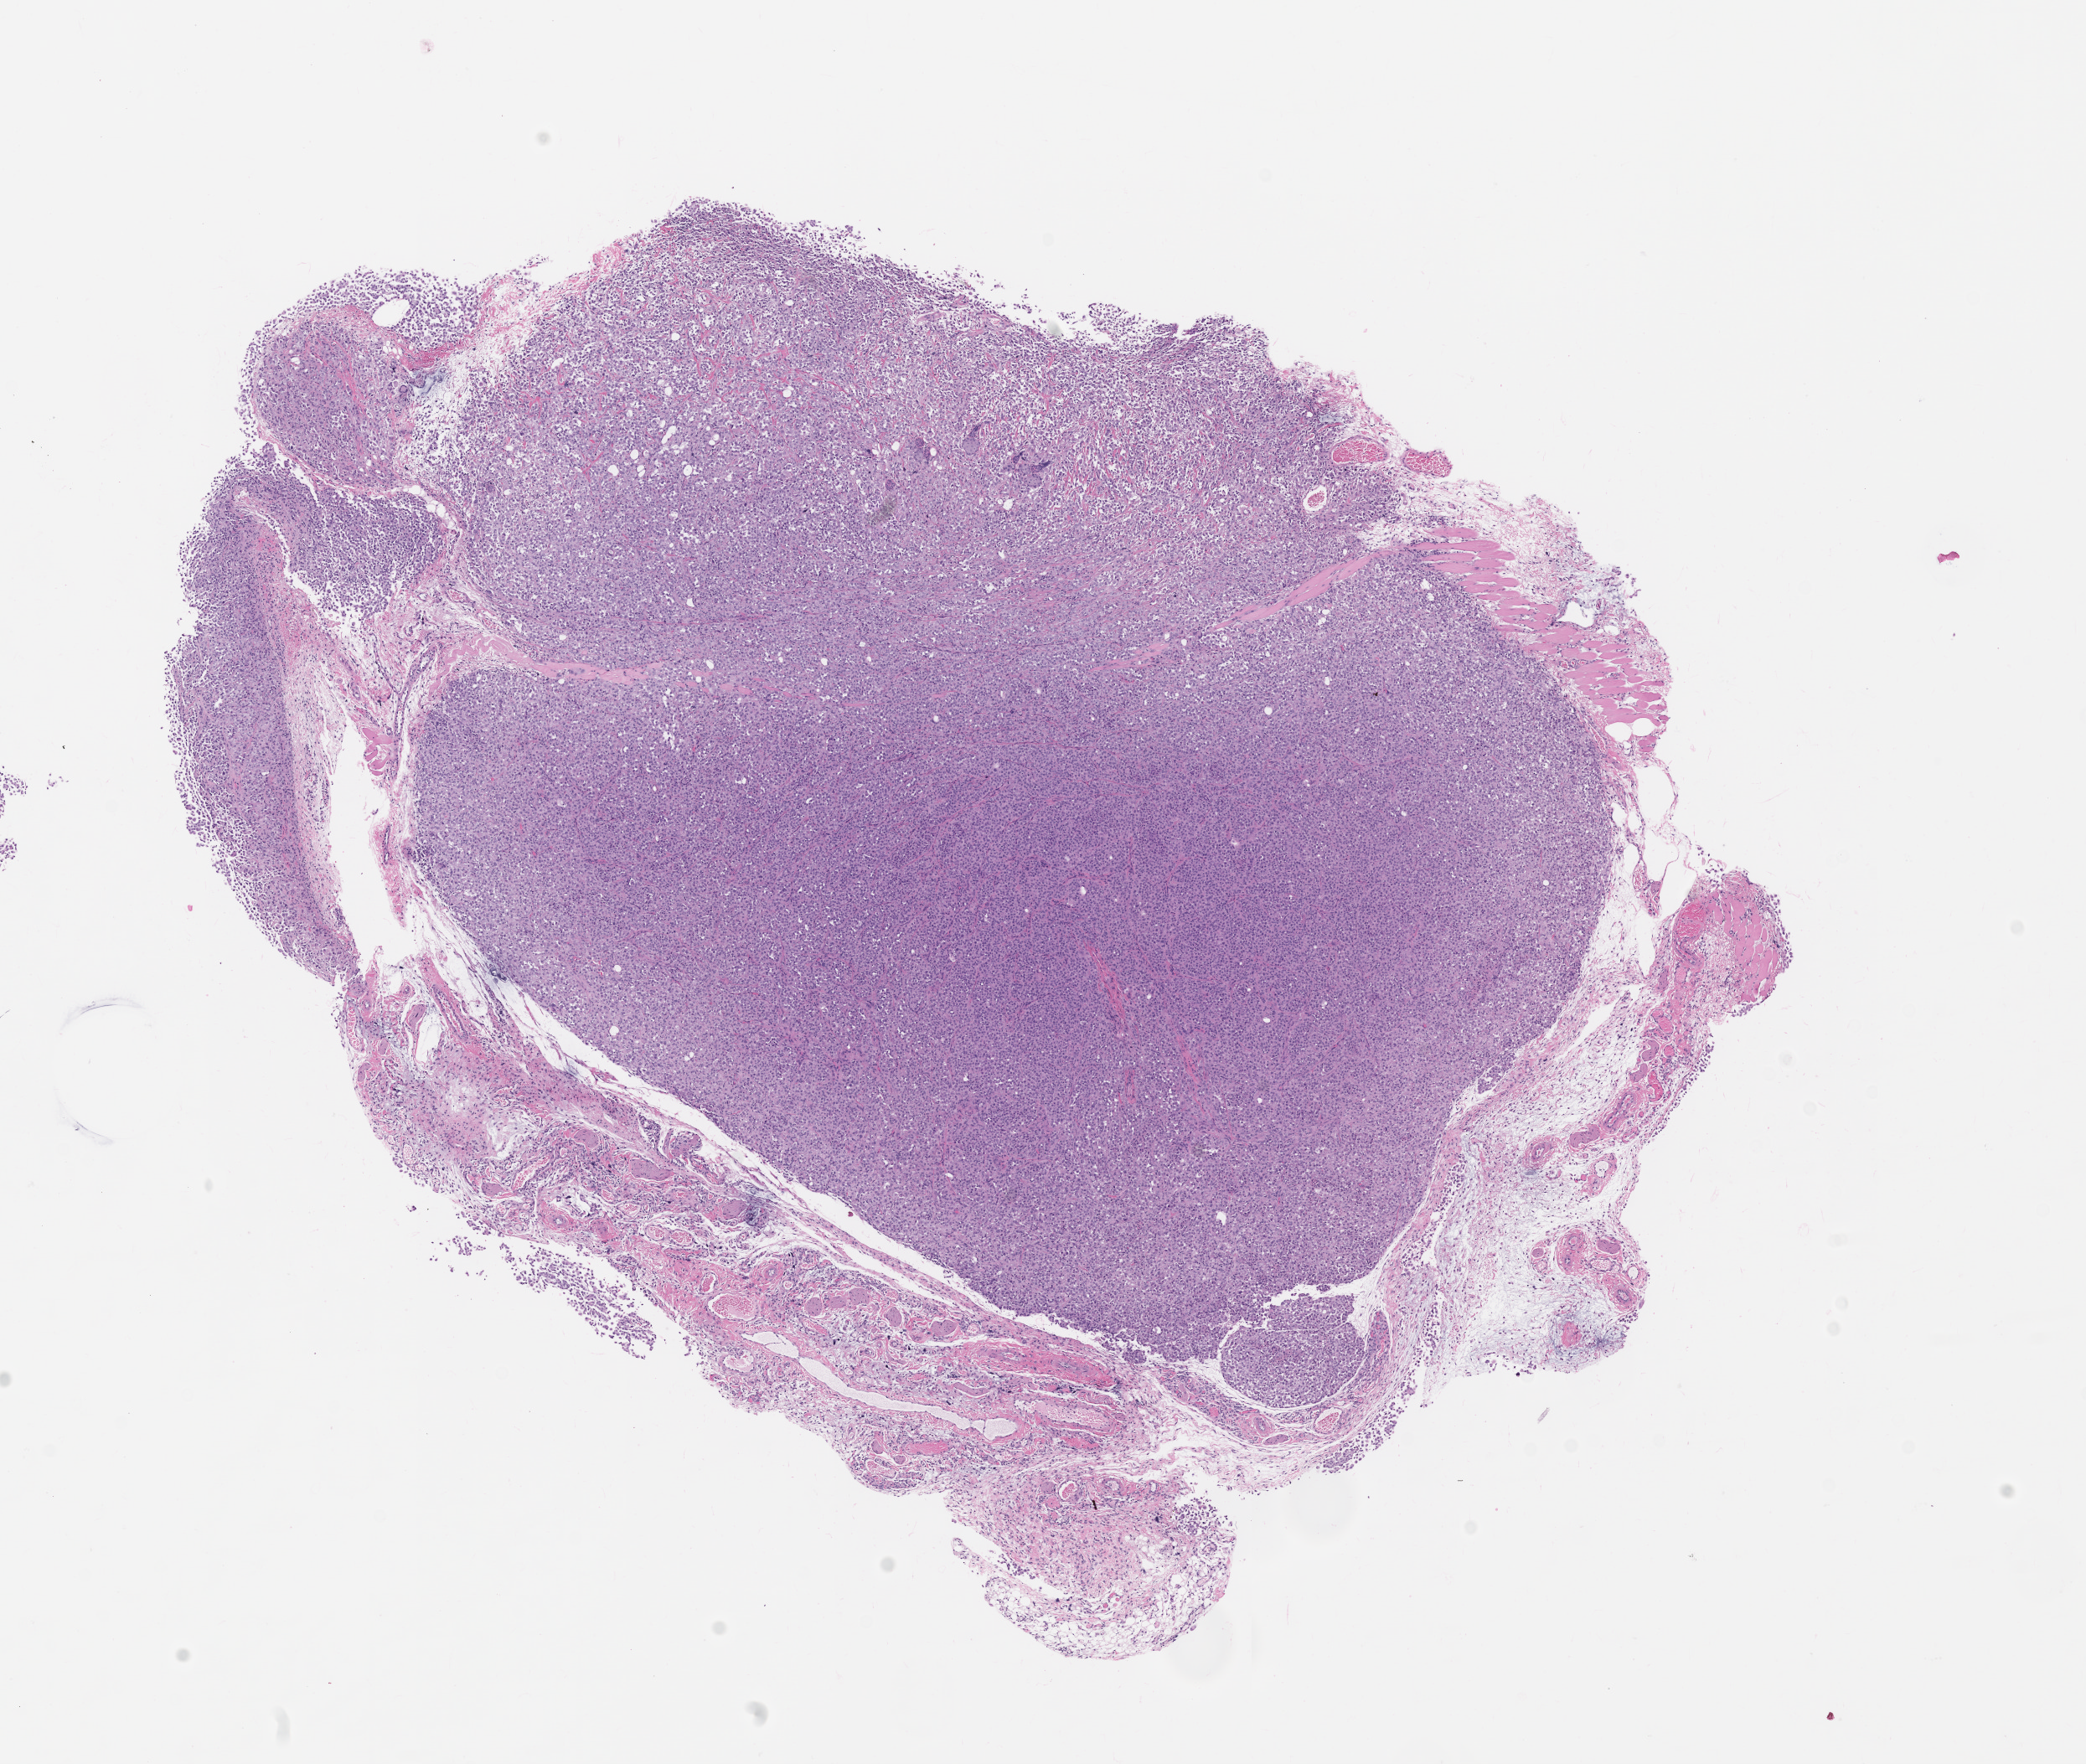
Whole-slide image, H&E: patient-derived xenograft (human tumor grown in a mouse), passage 1, a low-resolution overview of the entire scanned area, about 10.0 x 8.5 mm; formalin-fixed, paraffin-embedded (FFPE) tissue.
Originating patient diagnosis: Mesothelial Neoplasm.